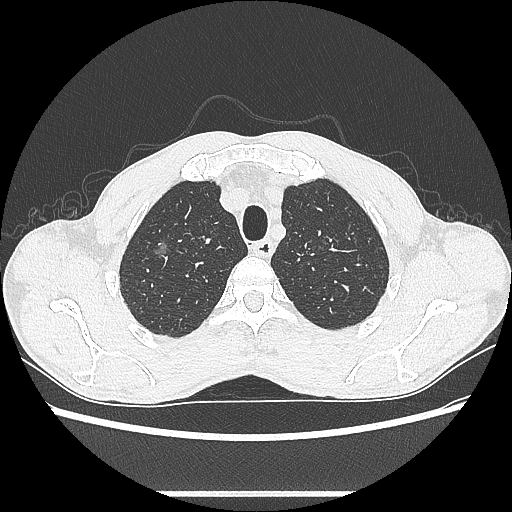
Chest CT, one axial slice; reconstruction kernel LUNG; 100 kVp; lung window (W 1500 / L -600 HU); 0.62 mm slice thickness; 512 × 512 image matrix. Patient: male, 54 years. From the clinical record (not read from this slice): clinical TNM (as recorded): T1a N0 M0.
Outlined on this slice (rectangle marked by the reading radiologist):
- lung tumour (recorded histology: adenocarcinoma): box from (x=151, y=232) to (x=175, y=265) px